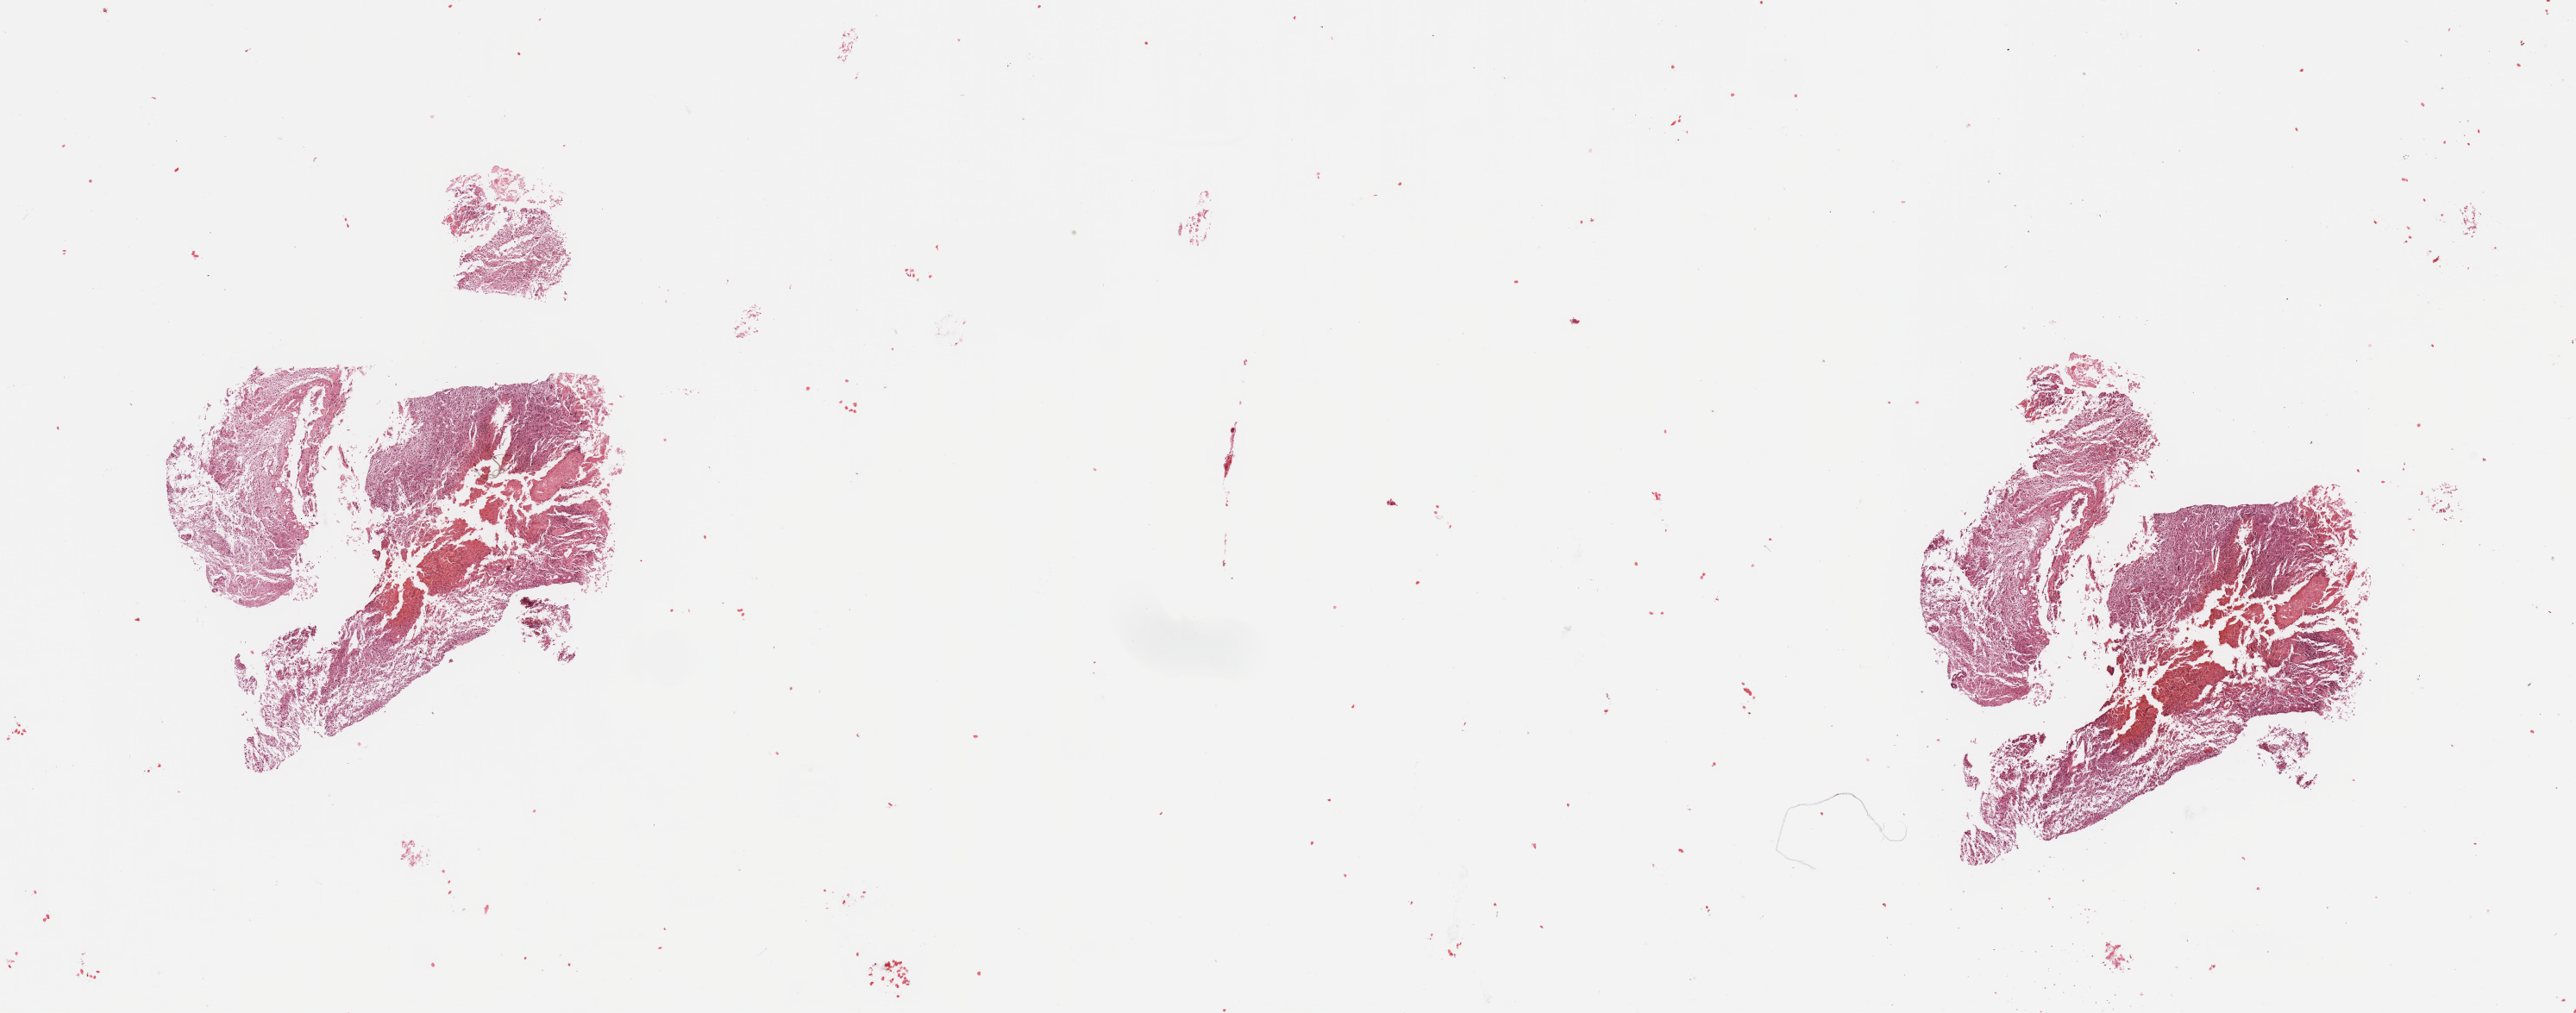
Digitized Hematoxylin and eosin (H&E) stained tissue section (whole slide) — shown as a low-resolution overview of the whole scanned area (about 23.6 x 9.3 mm, slide scanned at 20x), tumour tissue sample, brain. Patient: male, age 49 years.
- diagnosis: Glioblastoma
- primary tumour site (as recorded): temporal lobe